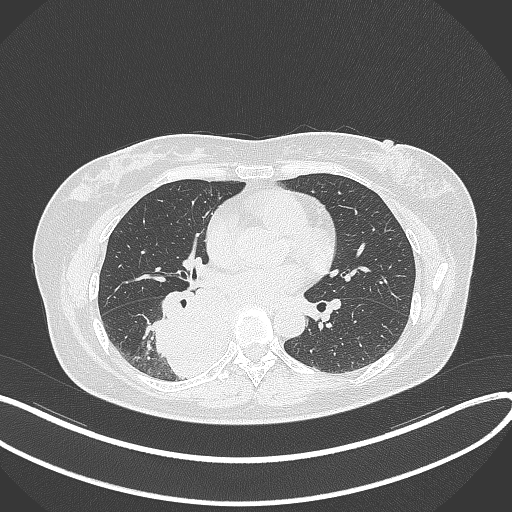
Chest CT, one axial slice. Position 172 of 331 along the scan axis. Lung window (W 1500 / L -600 HU). 1 mm slice thickness. 512 × 512 image matrix, field of view 400 × 400 mm. Patient: female, 54 years. Case-level facts recorded for this patient, not image findings: clinical TNM (as recorded): T4 N0 M0.
Structures marked on this image (rectangle marked by the reading radiologist):
- lung tumour (recorded histology: adenocarcinoma): bounding box <154,289,226,380> (left, top, right, bottom; pixels)